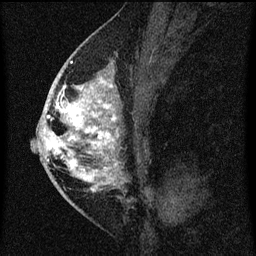
Breast MRI (dynamic contrast-enhanced), one sagittal slice. Dynamic contrast-enhanced series, image 2 of 3 at this slice position (ordered by acquisition). 1.5 T. TE 4.2 ms, TR 8 ms. 2 mm slice thickness. 256 × 256 image matrix, field of view 180 × 180 mm. Patient: female, 46 years.
Structures marked on this image (semi-automatically segmented with operator editing):
- analysis volume of interest (the breast-tissue region the enhancement analysis was run in; not a lesion): bounding box (x1, y1, x2, y2) in pixels: (48, 68, 120, 195)
- tumour enhancement mask (voxels above the 70 % enhancement threshold inside the analysis volume of interest): (48, 70, 119, 193)